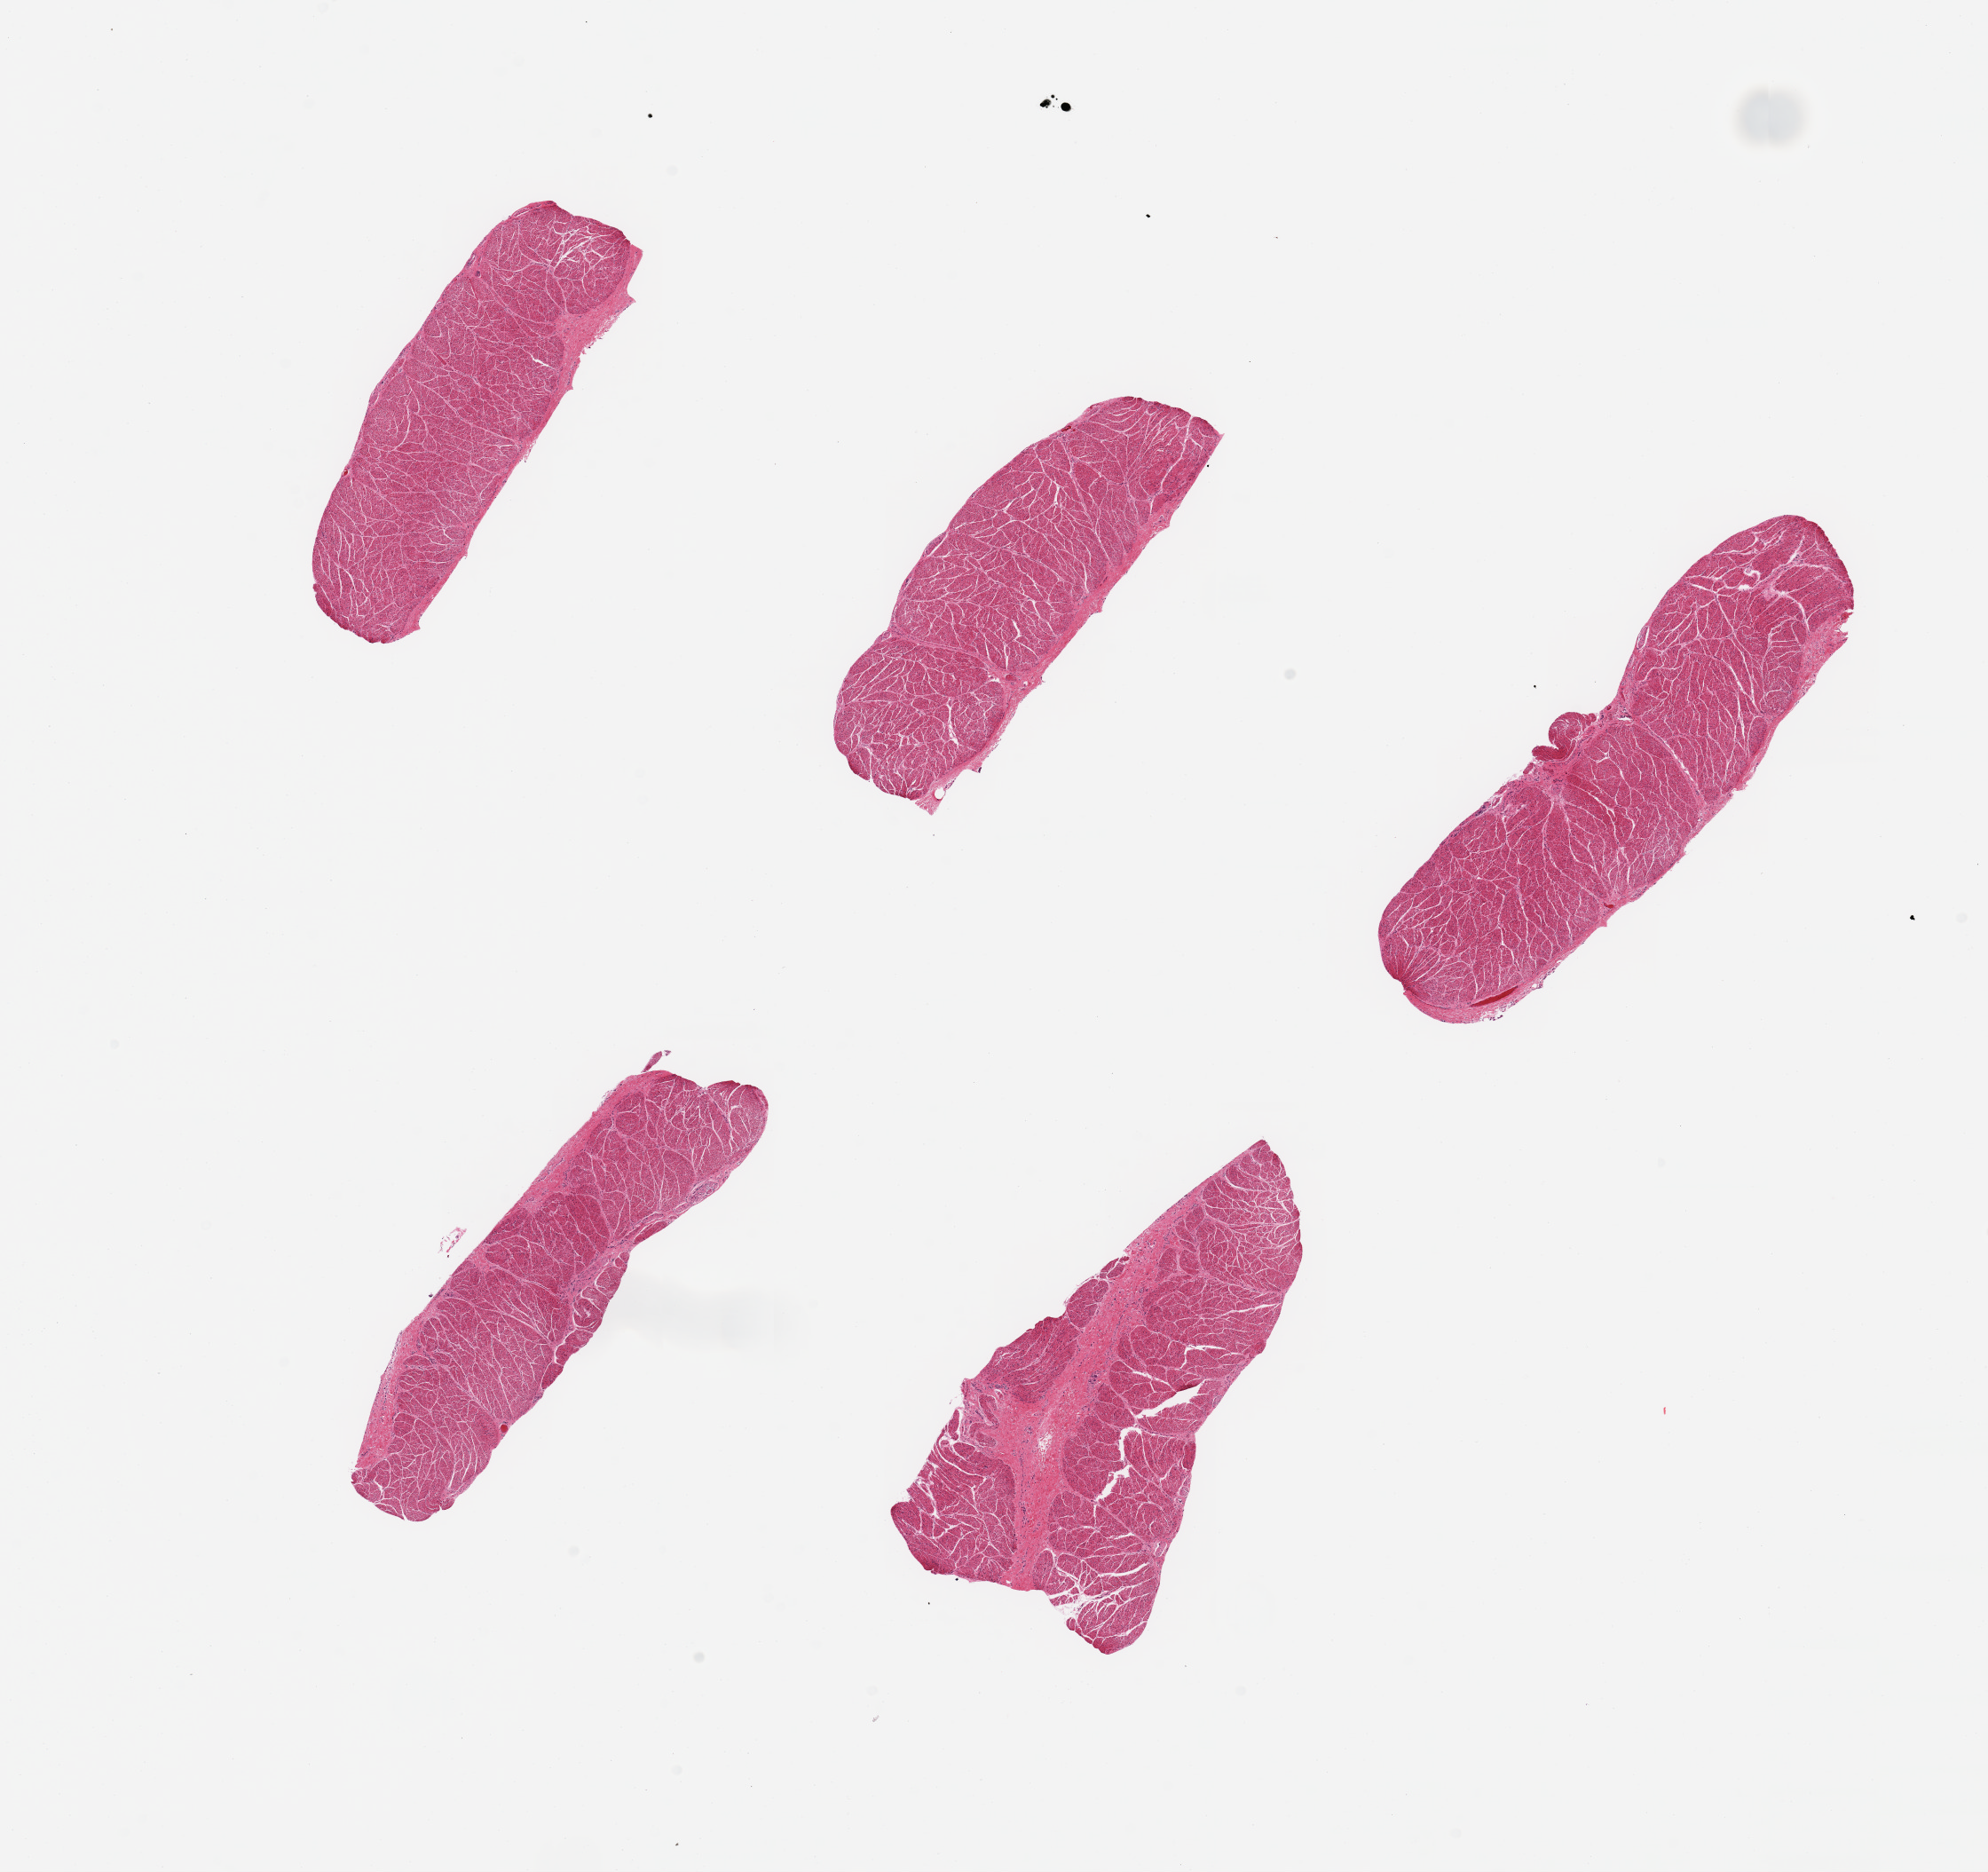
Whole-slide image, hematoxylin and eosin (H&E) stain — a low-resolution overview of the entire scanned area, about 17.7 x 16.7 mm; PAXgene-fixed, paraffin-embedded tissue; section of esophageal muscle (target tissue); donor tissue sample.
• pathologist's review note for this sample: 5 pieces; well dissected except 1 piece has 20% fibrous stroma